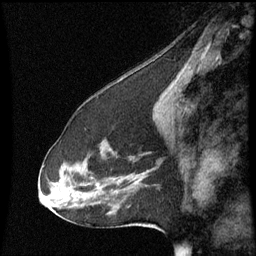
Breast MRI (dynamic contrast-enhanced), one sagittal slice. Position 28 of 60 along the scan axis. Dynamic contrast-enhanced series, image 2 of 3 at this slice position (ordered by acquisition). 1.5 T. TE 4.2 ms, TR 8.9 ms. 2.2 mm slice thickness. 256 × 256 image matrix, field of view 200 × 200 mm. Patient: female, 53 years. Case-level facts recorded for this patient, not image findings: setting: breast cancer imaged before/during neoadjuvant chemotherapy; receptor status: HR-positive, HER2-negative.
Annotated regions visible in this slice (semi-automatic segmentation, software-assisted and operator-edited):
- analysis volume of interest (the breast-tissue region the enhancement analysis was run in; not a lesion): bounding box (x1, y1, x2, y2) in pixels: (44, 120, 167, 223)
- tumour enhancement mask (voxels above the 70 % enhancement threshold inside the analysis volume of interest): (134, 180, 139, 185)